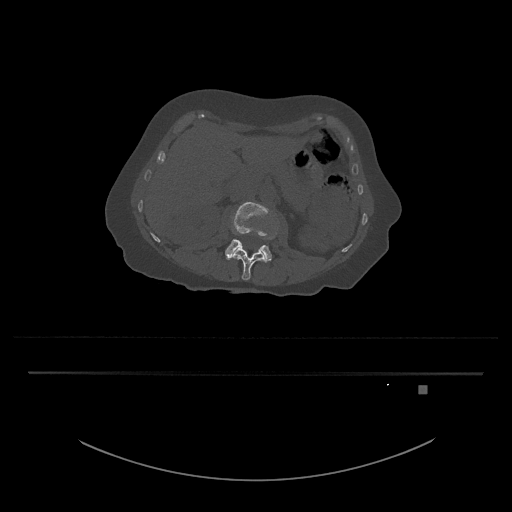
CT including the spine, one axial slice. Reconstruction kernel Br40s/3. Bone window (W 1800 / L 400 HU). 0.5 mm slice thickness. 512 × 512 image matrix. Female patient, age 57 years. Case-level facts recorded for this patient, not image findings: primary cancer: cervical.
Annotated regions visible in this slice (semi-automatically segmented with operator editing):
- L3 vertebra: box from (x=225, y=201) to (x=278, y=263) px